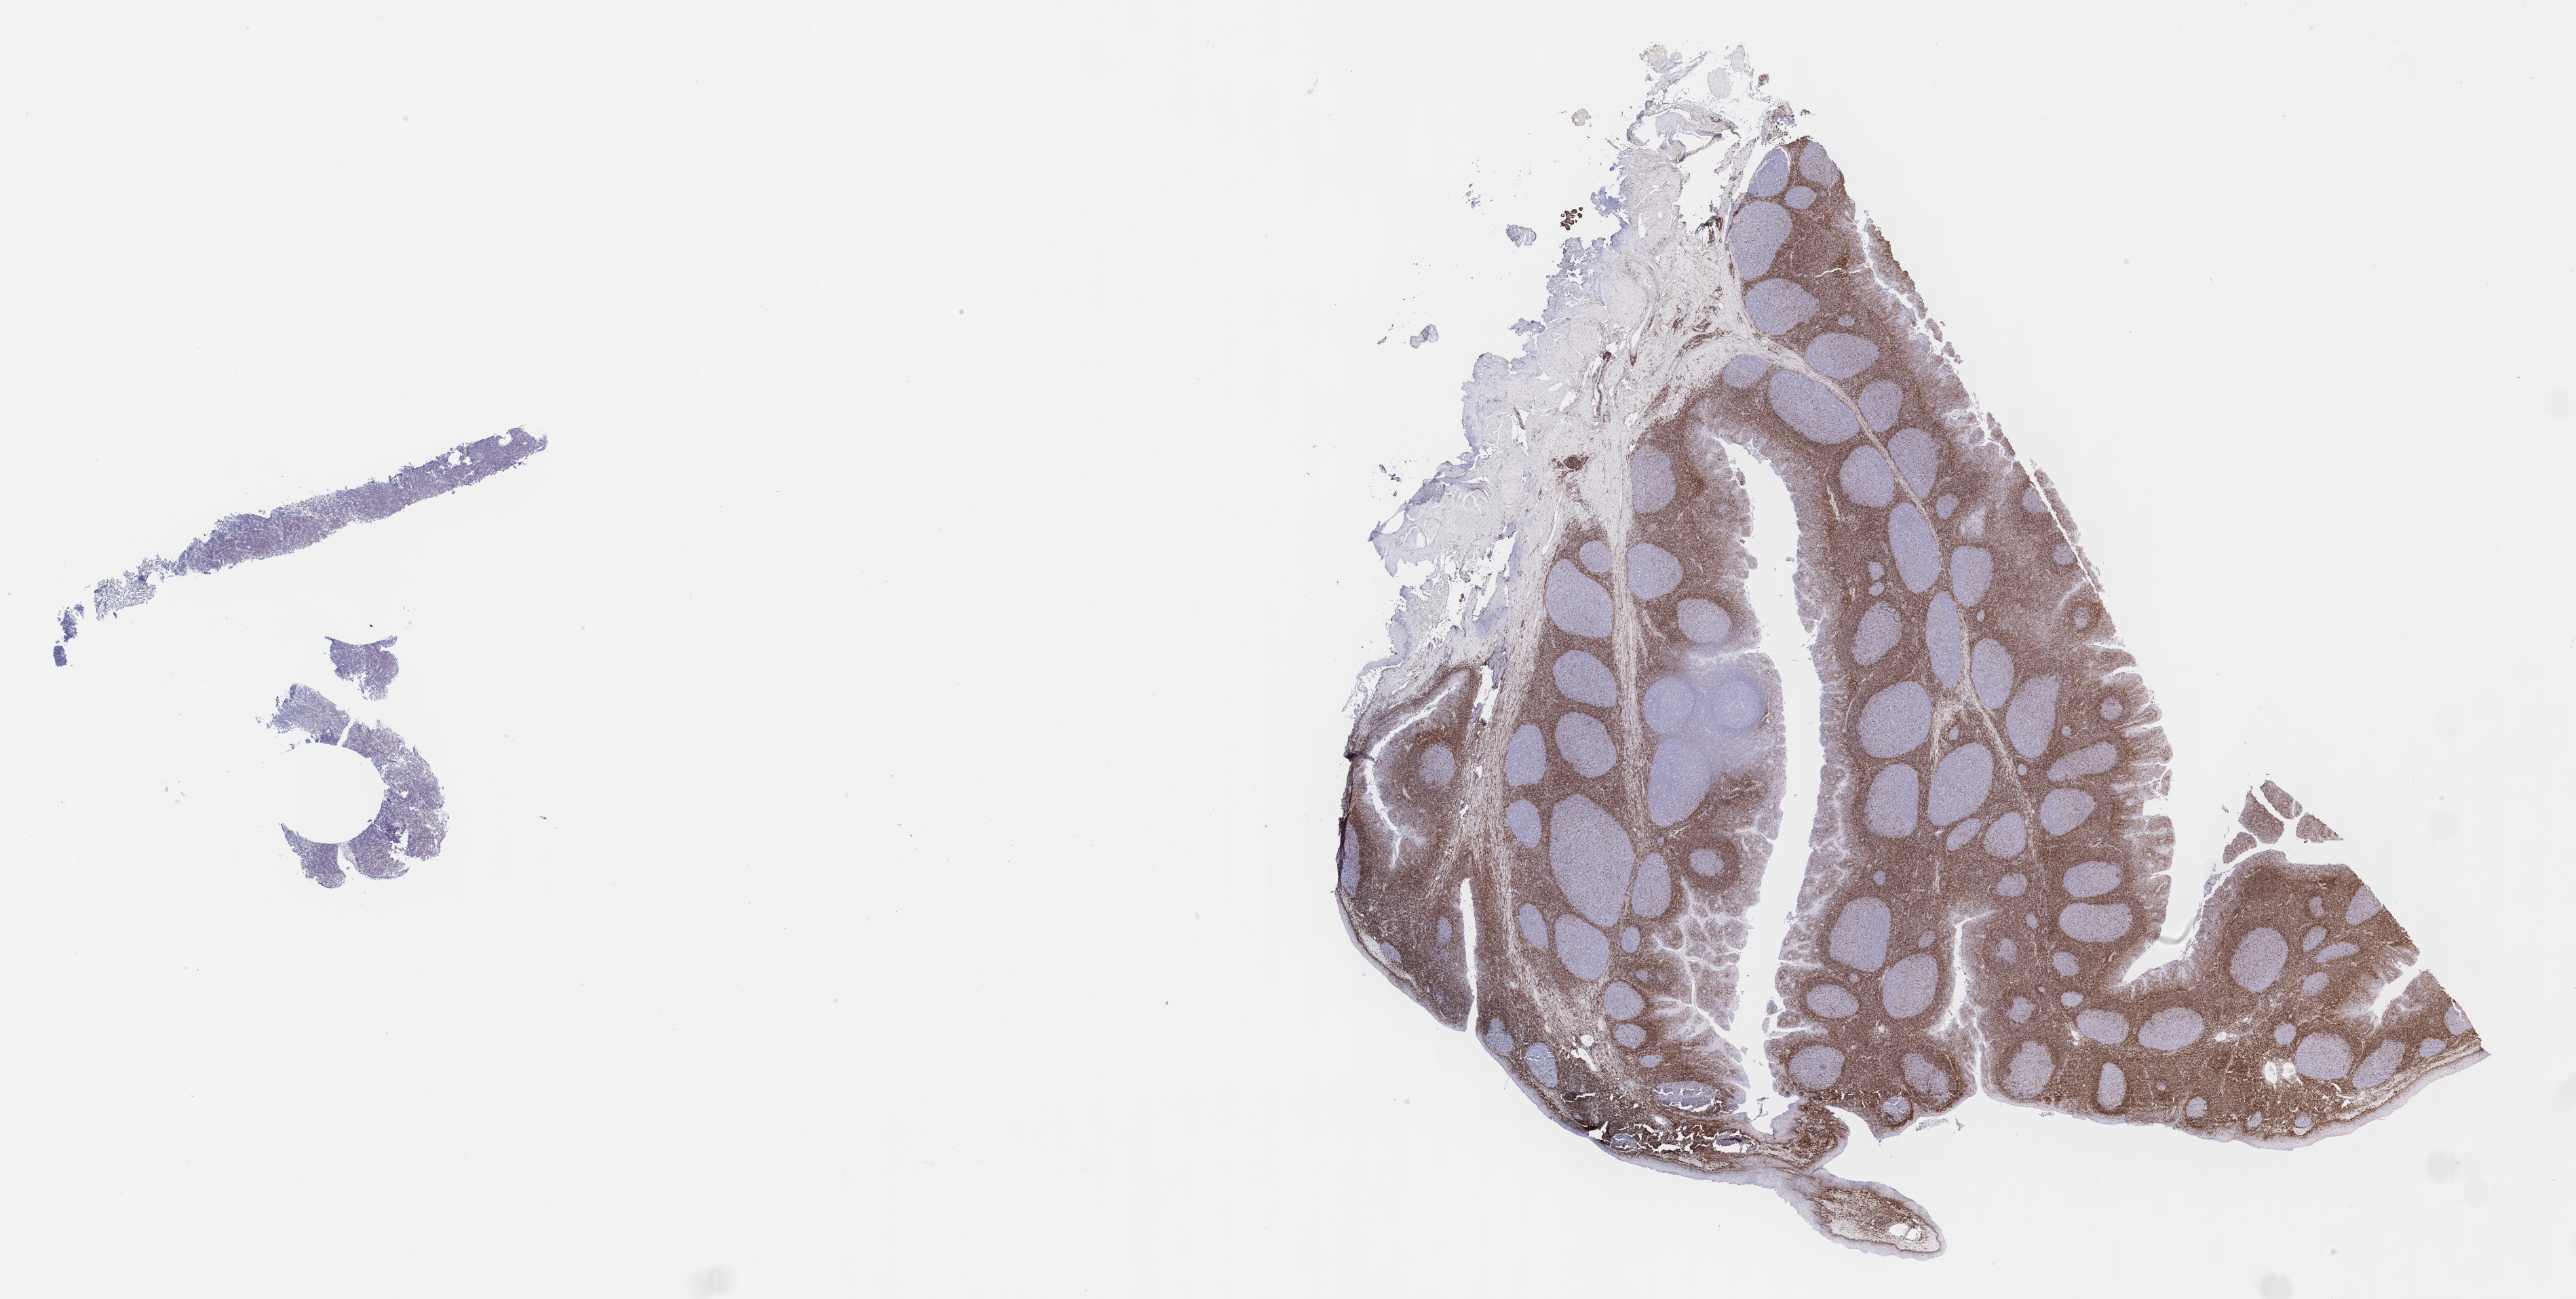
Immunohistochemistry (IHC) whole-slide image stained for BCL2 — a low-resolution overview of the entire scanned area, about 30.7 x 15.5 mm, specimen: tumor tissue, anatomic site: ovary. Patient female; age 10 years.
Histologic diagnosis: Burkitt lymphoma, NOS.